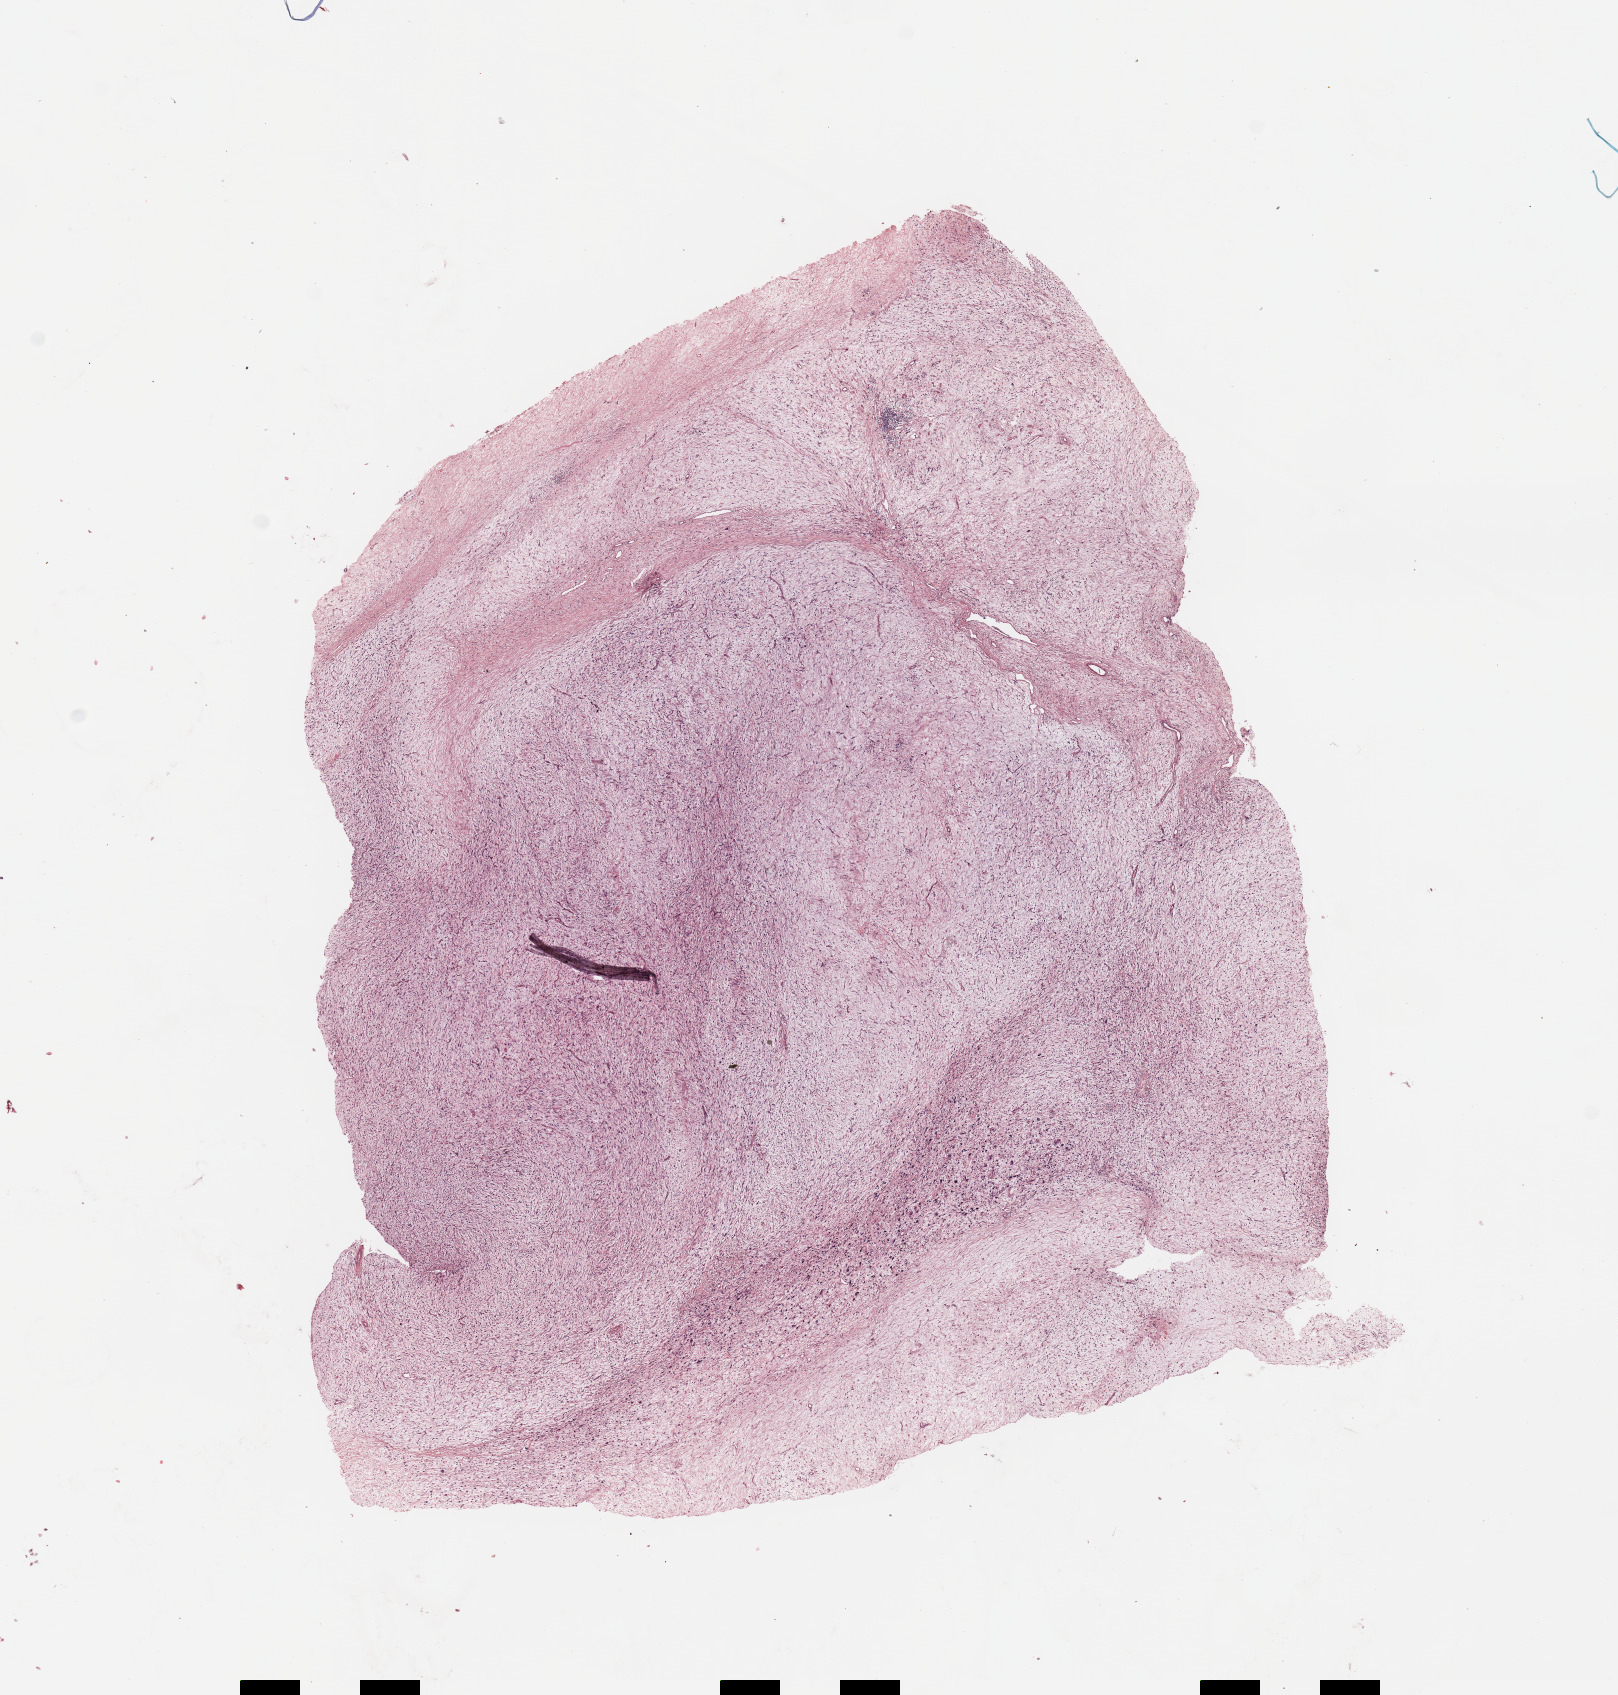
Whole-slide histology image, Hematoxylin and eosin (H&E) stained, whole scanned area (about 12.8 x 13.4 mm) shown as a low-resolution overview, tumour tissue sample. Patient: female, age 77 years.
Patient diagnosis (cohort enrolment): sarcoma (site not recorded at cohort level). Primary tumour site (as recorded): lower extremity.